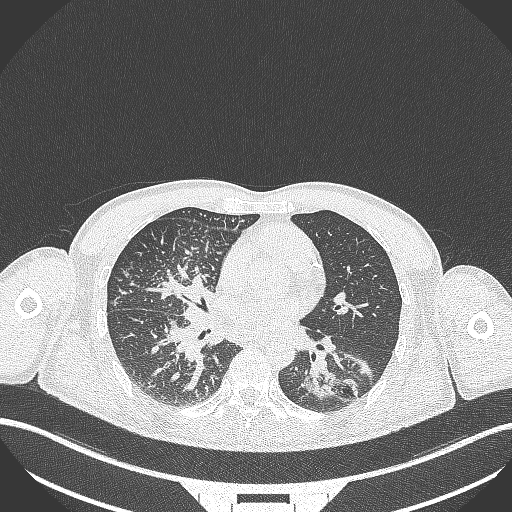
Chest CT, one axial slice. Position 152 of 348 along the scan axis. Reconstruction kernel B70f. Lung window (W 1500 / L -600 HU). 1 mm slice thickness. 512 × 512 image matrix, field of view 400 × 400 mm. Male patient, age 49 years. Case-level facts recorded for this patient, not image findings: clinical TNM (as recorded): T2b N1 M0.
Outlined on this slice (bounding box drawn by a radiologist):
- lung tumour (recorded histology: adenocarcinoma): bounding box [x1, y1, x2, y2] px = [302, 360, 359, 404]